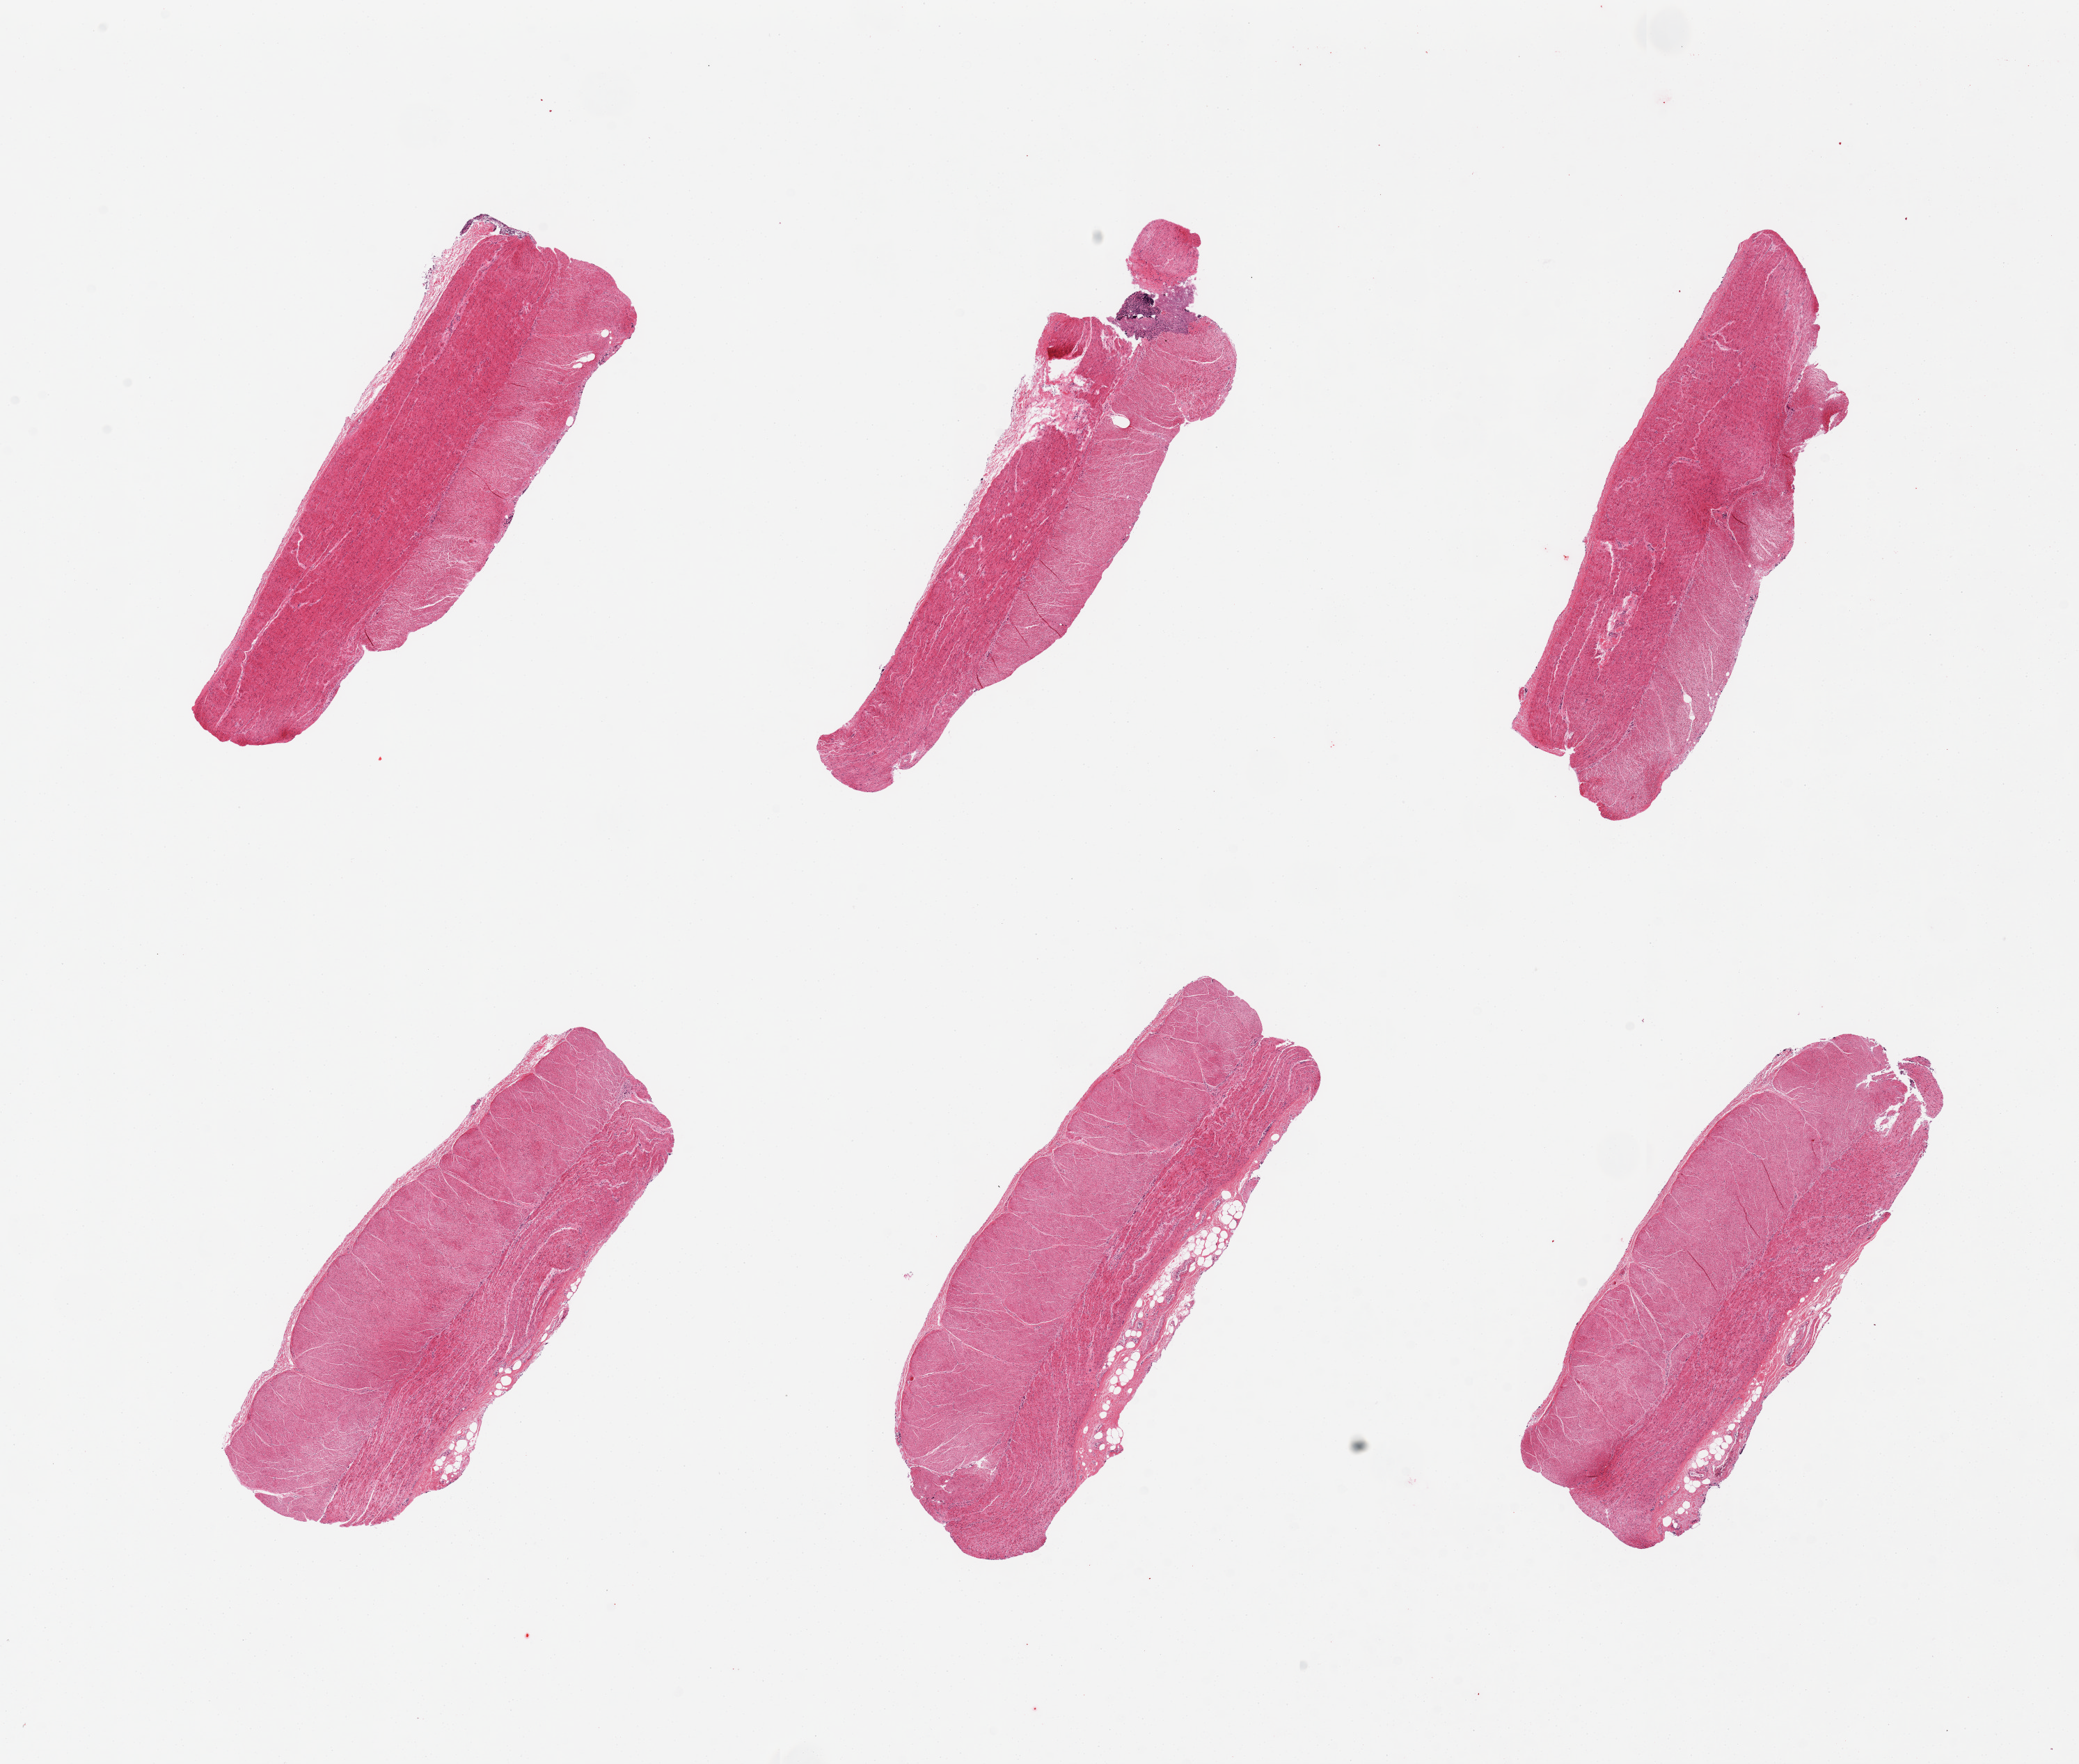
Whole-slide image, haematoxylin and eosin stain, shown as a low-resolution overview of the whole scanned area (about 23.6 x 20.0 mm, from a 20x scan), PAXgene-fixed, paraffin-embedded tissue, target tissue: sigmoid colon, tissue donor sample. Male donor.
Reviewer comment on this tissue sample: 6 pieces; well trimmed muscle.